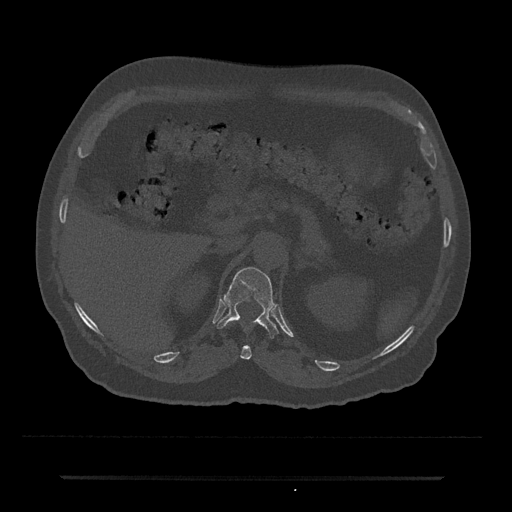
CT including the spine, one axial slice. Reconstruction kernel Br40s/3. Bone window (W 1800 / L 400 HU). 0.5 mm slice thickness. 512 × 512 image matrix. Patient: male, 69 years. From the clinical record (not read from this slice): primary cancer: prostate.
Outlined on this slice (semi-automatic segmentation, software-assisted and operator-edited):
- T11 vertebra: box from (x=231, y=321) to (x=252, y=360) px
- T12 vertebra: (x=216, y=267)–(x=278, y=338)